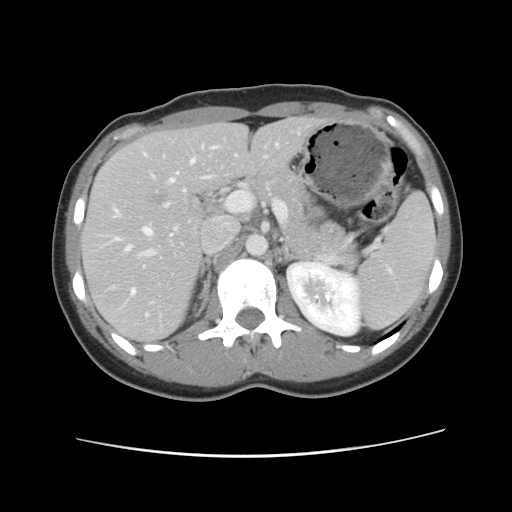
Contrast-enhanced abdominal CT, one axial slice; position 62 of 134 along the scan axis; 120 kVp; intravenous contrast given; soft-tissue window (W 400 / L 40 HU); 512 × 512 image matrix, field of view 339 × 339 mm. Female patient, age 33 years. From the clinical record (not read from this slice): diagnosis: colorectal cancer liver metastases, imaged before liver resection; multiple liver metastases: yes; largest metastasis: 4.5 cm; chemotherapy before resection: no.
Outlined on this slice (outlined manually by an expert reader):
- hepatic veins: bounding box [x1, y1, x2, y2] px = [115, 144, 278, 316]
- liver: [83, 118, 320, 342]
- planned liver remnant (the part of the liver to remain after resection): [83, 117, 321, 341]
- portal vein (with intrahepatic branches): [137, 195, 236, 303]
- liver metastasis: [144, 186, 174, 208]